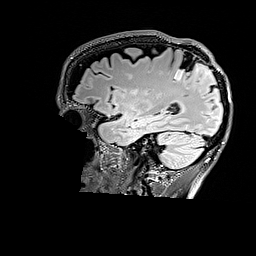
Brain MRI from a brain-tumour surgery series, one sagittal slice; position 120 of 176 along the scan axis; T2 FLAIR; 256 × 256 image matrix. From the clinical record (not read from this slice): histopathology: Astrocytoma; WHO grade: 3; IDH mutation: yes; tumour location: Right Parietal.
Annotated regions visible in this slice (expert manual segmentation):
- tumour: bounding box <174,63,211,80> (left, top, right, bottom; pixels)
- tumour: <206,75,211,80>